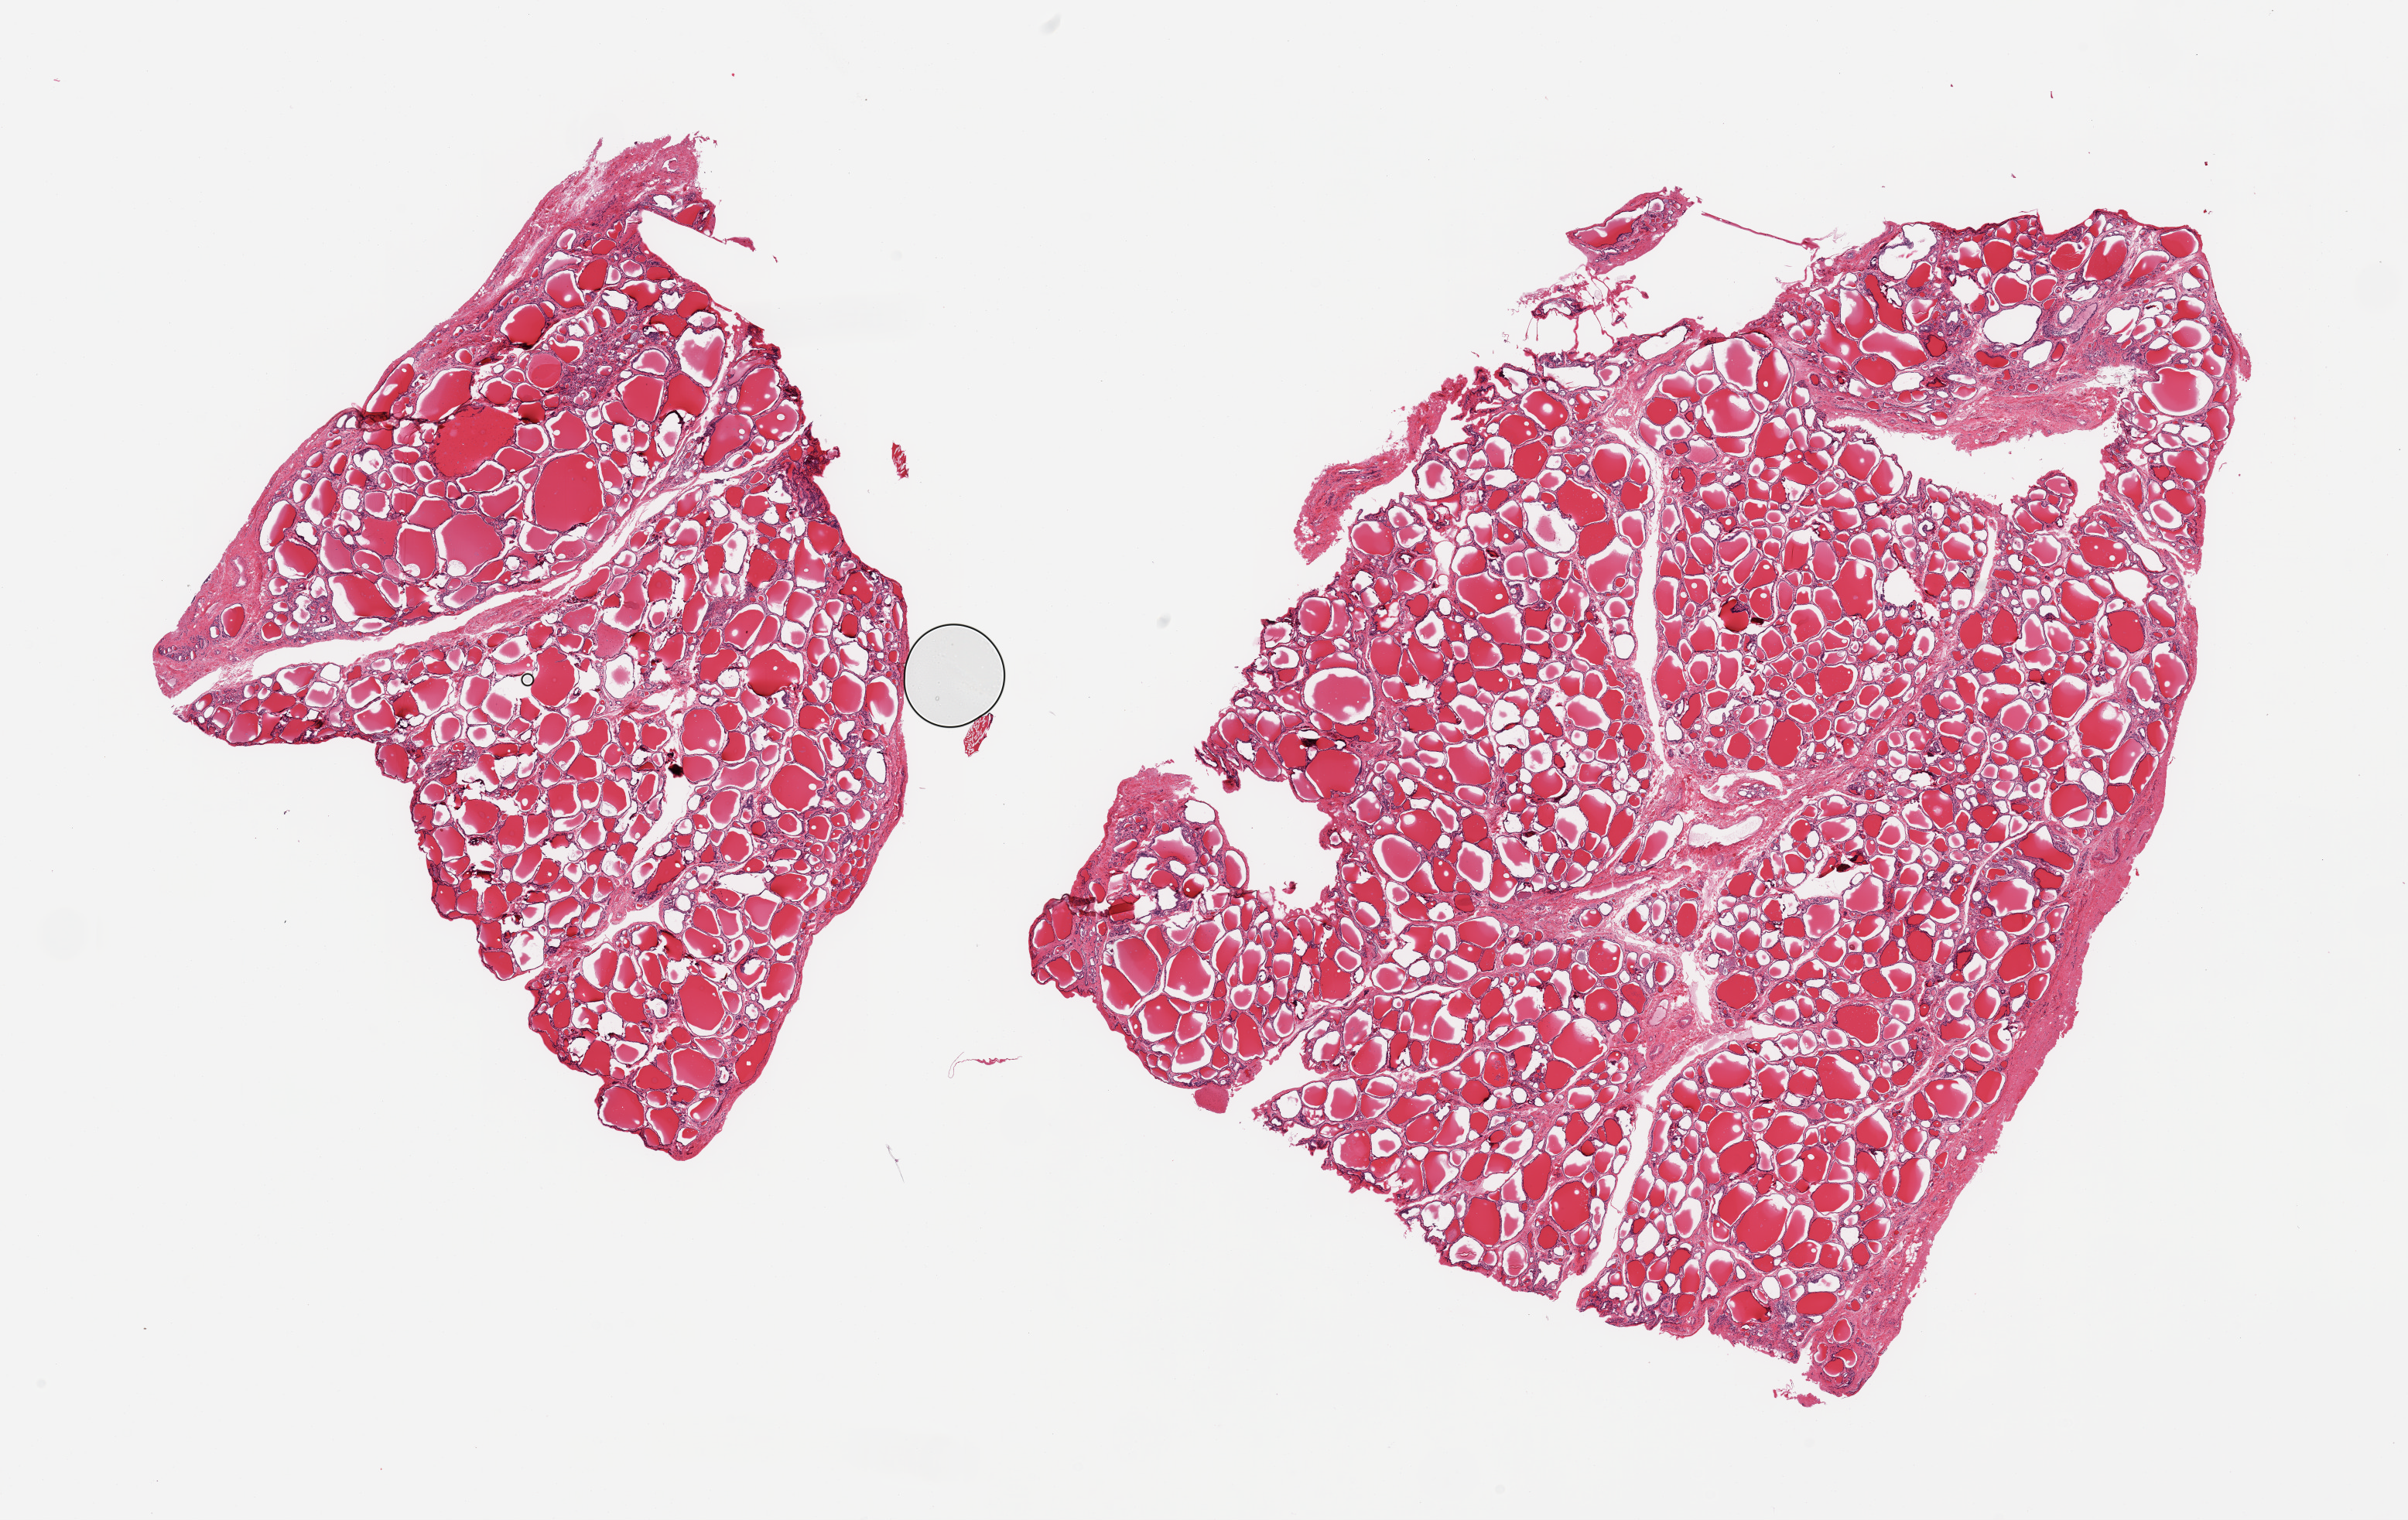
Digitized haematoxylin and eosin-stained section, brightfield — whole scanned area (about 24.6 x 15.5 mm, slide scanned at 20x) shown as a low-resolution overview; PAXgene-fixed, paraffin-embedded tissue; section of thyroid (target tissue); donor tissue sample. Donor sex: male.
Pathologist's review note for this sample: 2 pieces, no abnormalities.